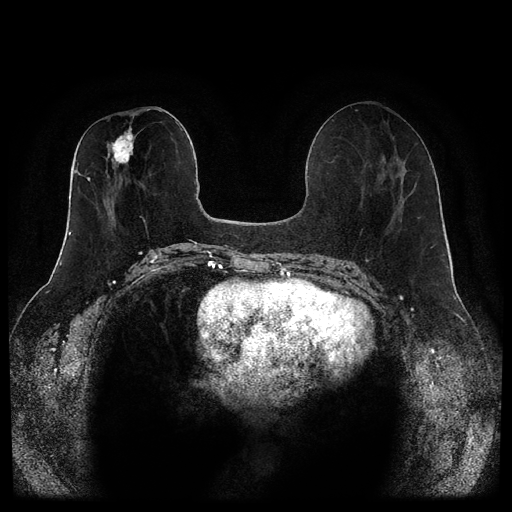
Breast MRI (dynamic contrast-enhanced, multi-phase), one axial slice; slice 46 of 116 in the series (ordered by position); dynamic contrast-enhanced series, time point 2 of 5 at this slice position (early post-contrast); 1.5 T; TE 2.6 ms, TR 5.3 ms; 2 mm slice thickness; 512 × 512 image matrix, field of view 350 × 350 mm. Female patient, age 46 years.
Annotated regions visible in this slice (semi-automatic segmentation, software-assisted and operator-edited):
- breast lesion (labelled 'tumour' in the annotation; benign lesions carry a separate 'benign' label): bounding box (x1, y1, x2, y2) in pixels: (111, 114, 136, 167)